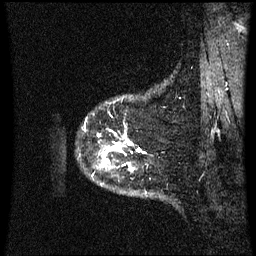
Breast MRI (dynamic contrast-enhanced), one sagittal slice. Slice 56 of 60 in the series (ordered by position). Dynamic contrast-enhanced series, image 2 of 3 at this slice position (ordered by acquisition). 1.5 T. TE 4.2 ms, TR 8.9 ms. 2.3 mm slice thickness. 256 × 256 image matrix, field of view 210 × 210 mm. Female patient, age 43 years. Case-level facts recorded for this patient, not image findings: setting: breast cancer imaged before/during neoadjuvant chemotherapy; receptor status: HER2-positive.
Structures marked on this image (semi-automatic segmentation, software-assisted and operator-edited):
- analysis volume of interest (the breast-tissue region the enhancement analysis was run in; not a lesion): bounding box [x1, y1, x2, y2] px = [85, 115, 147, 177]
- tumour enhancement mask (voxels above the 70 % enhancement threshold inside the analysis volume of interest): [99, 135, 142, 171]